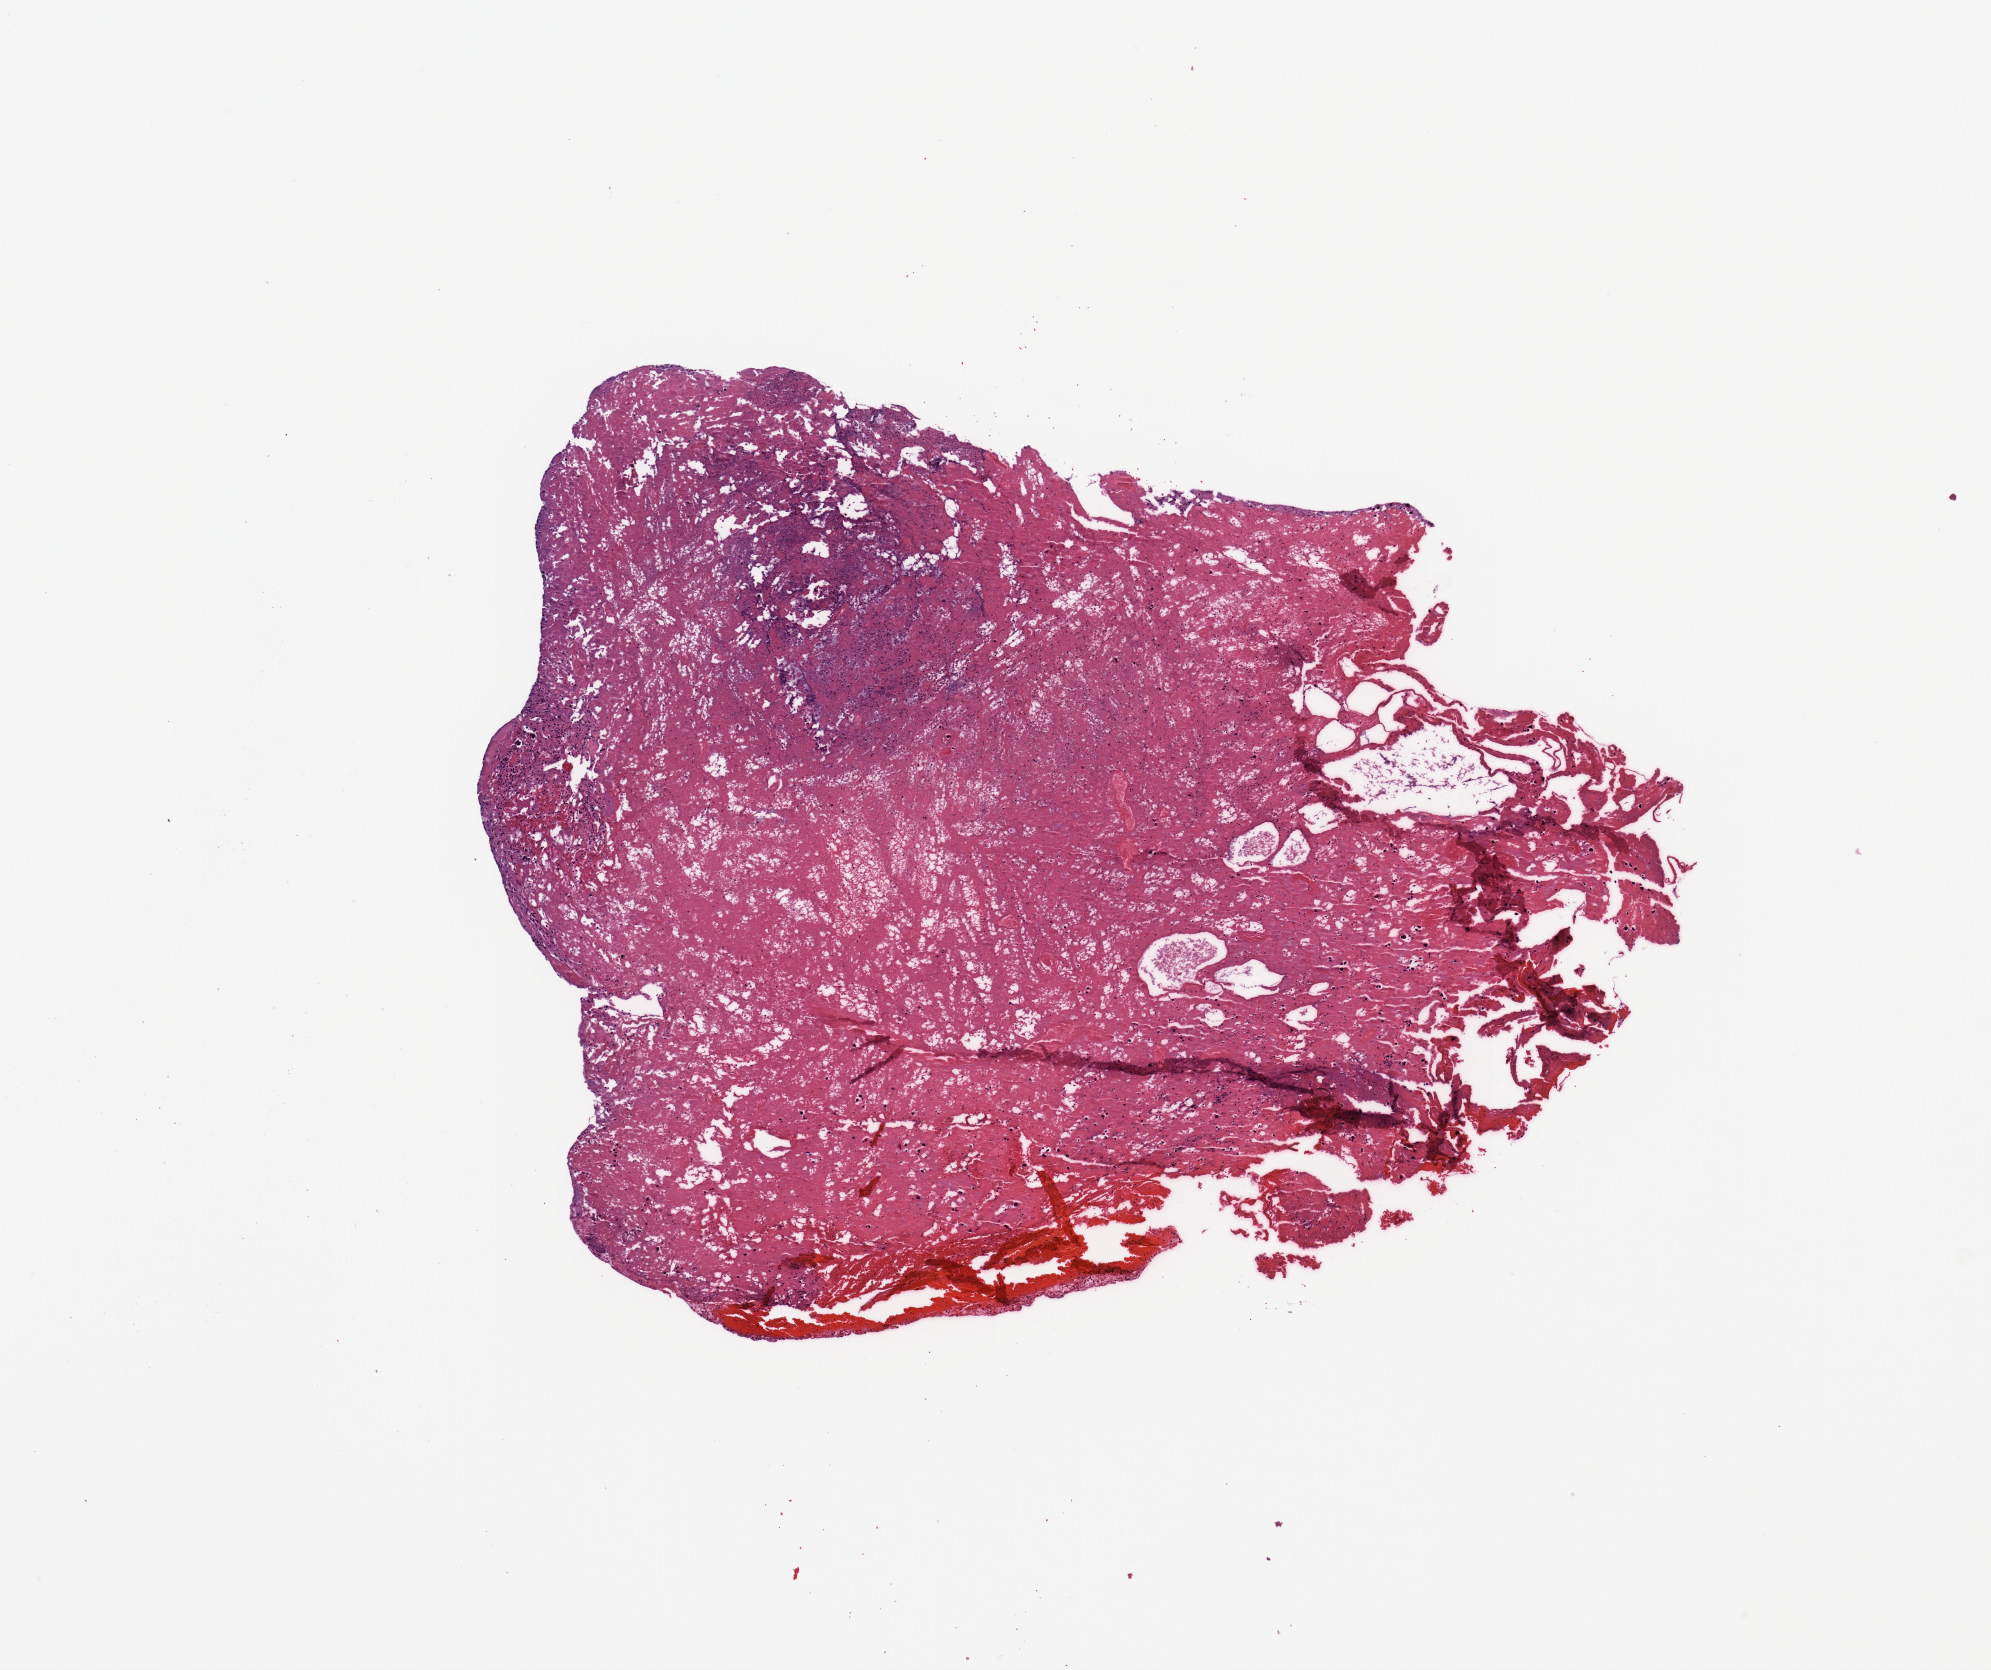
Whole-slide histology image, Hematoxylin and eosin (H&E) stained, shown as a low-resolution overview of the whole scanned area (about 7.9 x 6.6 mm, from a 20x scan); brain, tumour tissue. 59-year-old female patient.
Diagnosis: Glioblastoma. Primary tumour site (as recorded): frontal lobe.